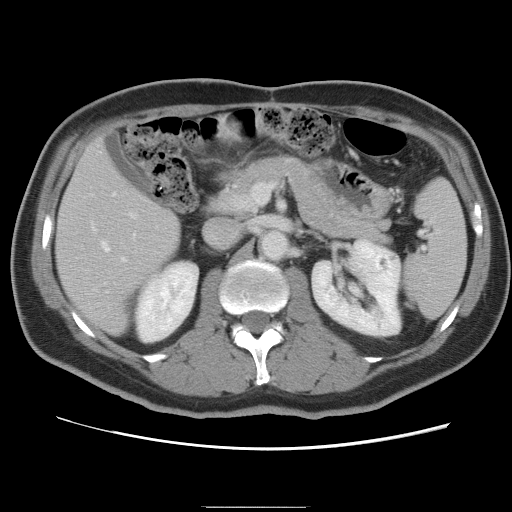
Contrast-enhanced abdominal CT, one axial slice. Slice 40 of 87 in the series (ordered by position). Intravenous contrast given. Soft-tissue window (W 400 / L 40 HU). 5 mm slice thickness. 512 × 512 image matrix. Male patient, age 63 years. From the clinical record (not read from this slice): diagnosis: colorectal cancer liver metastases, imaged before liver resection; multiple liver metastases: no; largest metastasis: 9 cm; disease in both lobes: no.
Structures marked on this image (manually delineated by an expert):
- hepatic veins: bounding box [x1, y1, x2, y2] px = [92, 193, 134, 251]
- liver: [58, 143, 180, 334]
- planned liver remnant (the part of the liver to remain after resection): [57, 145, 180, 334]
- portal vein (with intrahepatic branches): [106, 211, 138, 293]